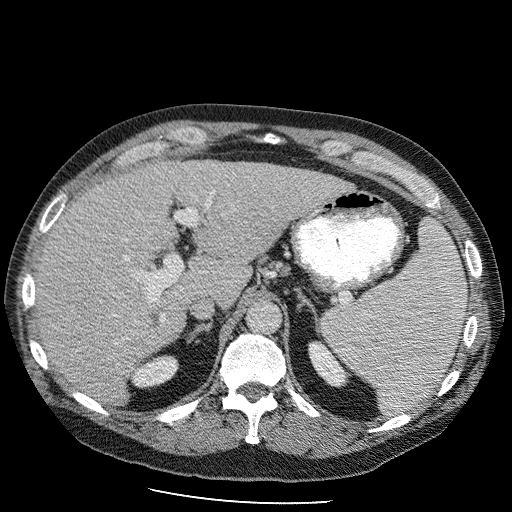
Contrast-enhanced abdominal CT (liver protocol), one axial slice; slice 66 of 98 in the series (ordered by position); reconstruction kernel STANDARD; 120 kVp; soft-tissue window (W 400 / L 40 HU); 2.5 mm slice thickness; 512 × 512 image matrix, field of view 400 × 400 mm. Case-level facts recorded for this patient, not image findings: diagnosis: hepatocellular carcinoma (patient treated with transarterial chemoembolisation; whether this scan precedes or follows treatment is not stated here); TNM stage (as recorded): Stage-II; Child-Pugh class: B; tumour differentiation: moderately differentiated.
Annotated regions visible in this slice (semi-automatic segmentation, software-assisted and operator-edited):
- liver parenchyma outside the tumour (the mass and vessels are separate outlines, so this box may not span the whole liver): box from (x=38, y=155) to (x=350, y=406) px
- liver vessels: (x=125, y=185)–(x=221, y=332)